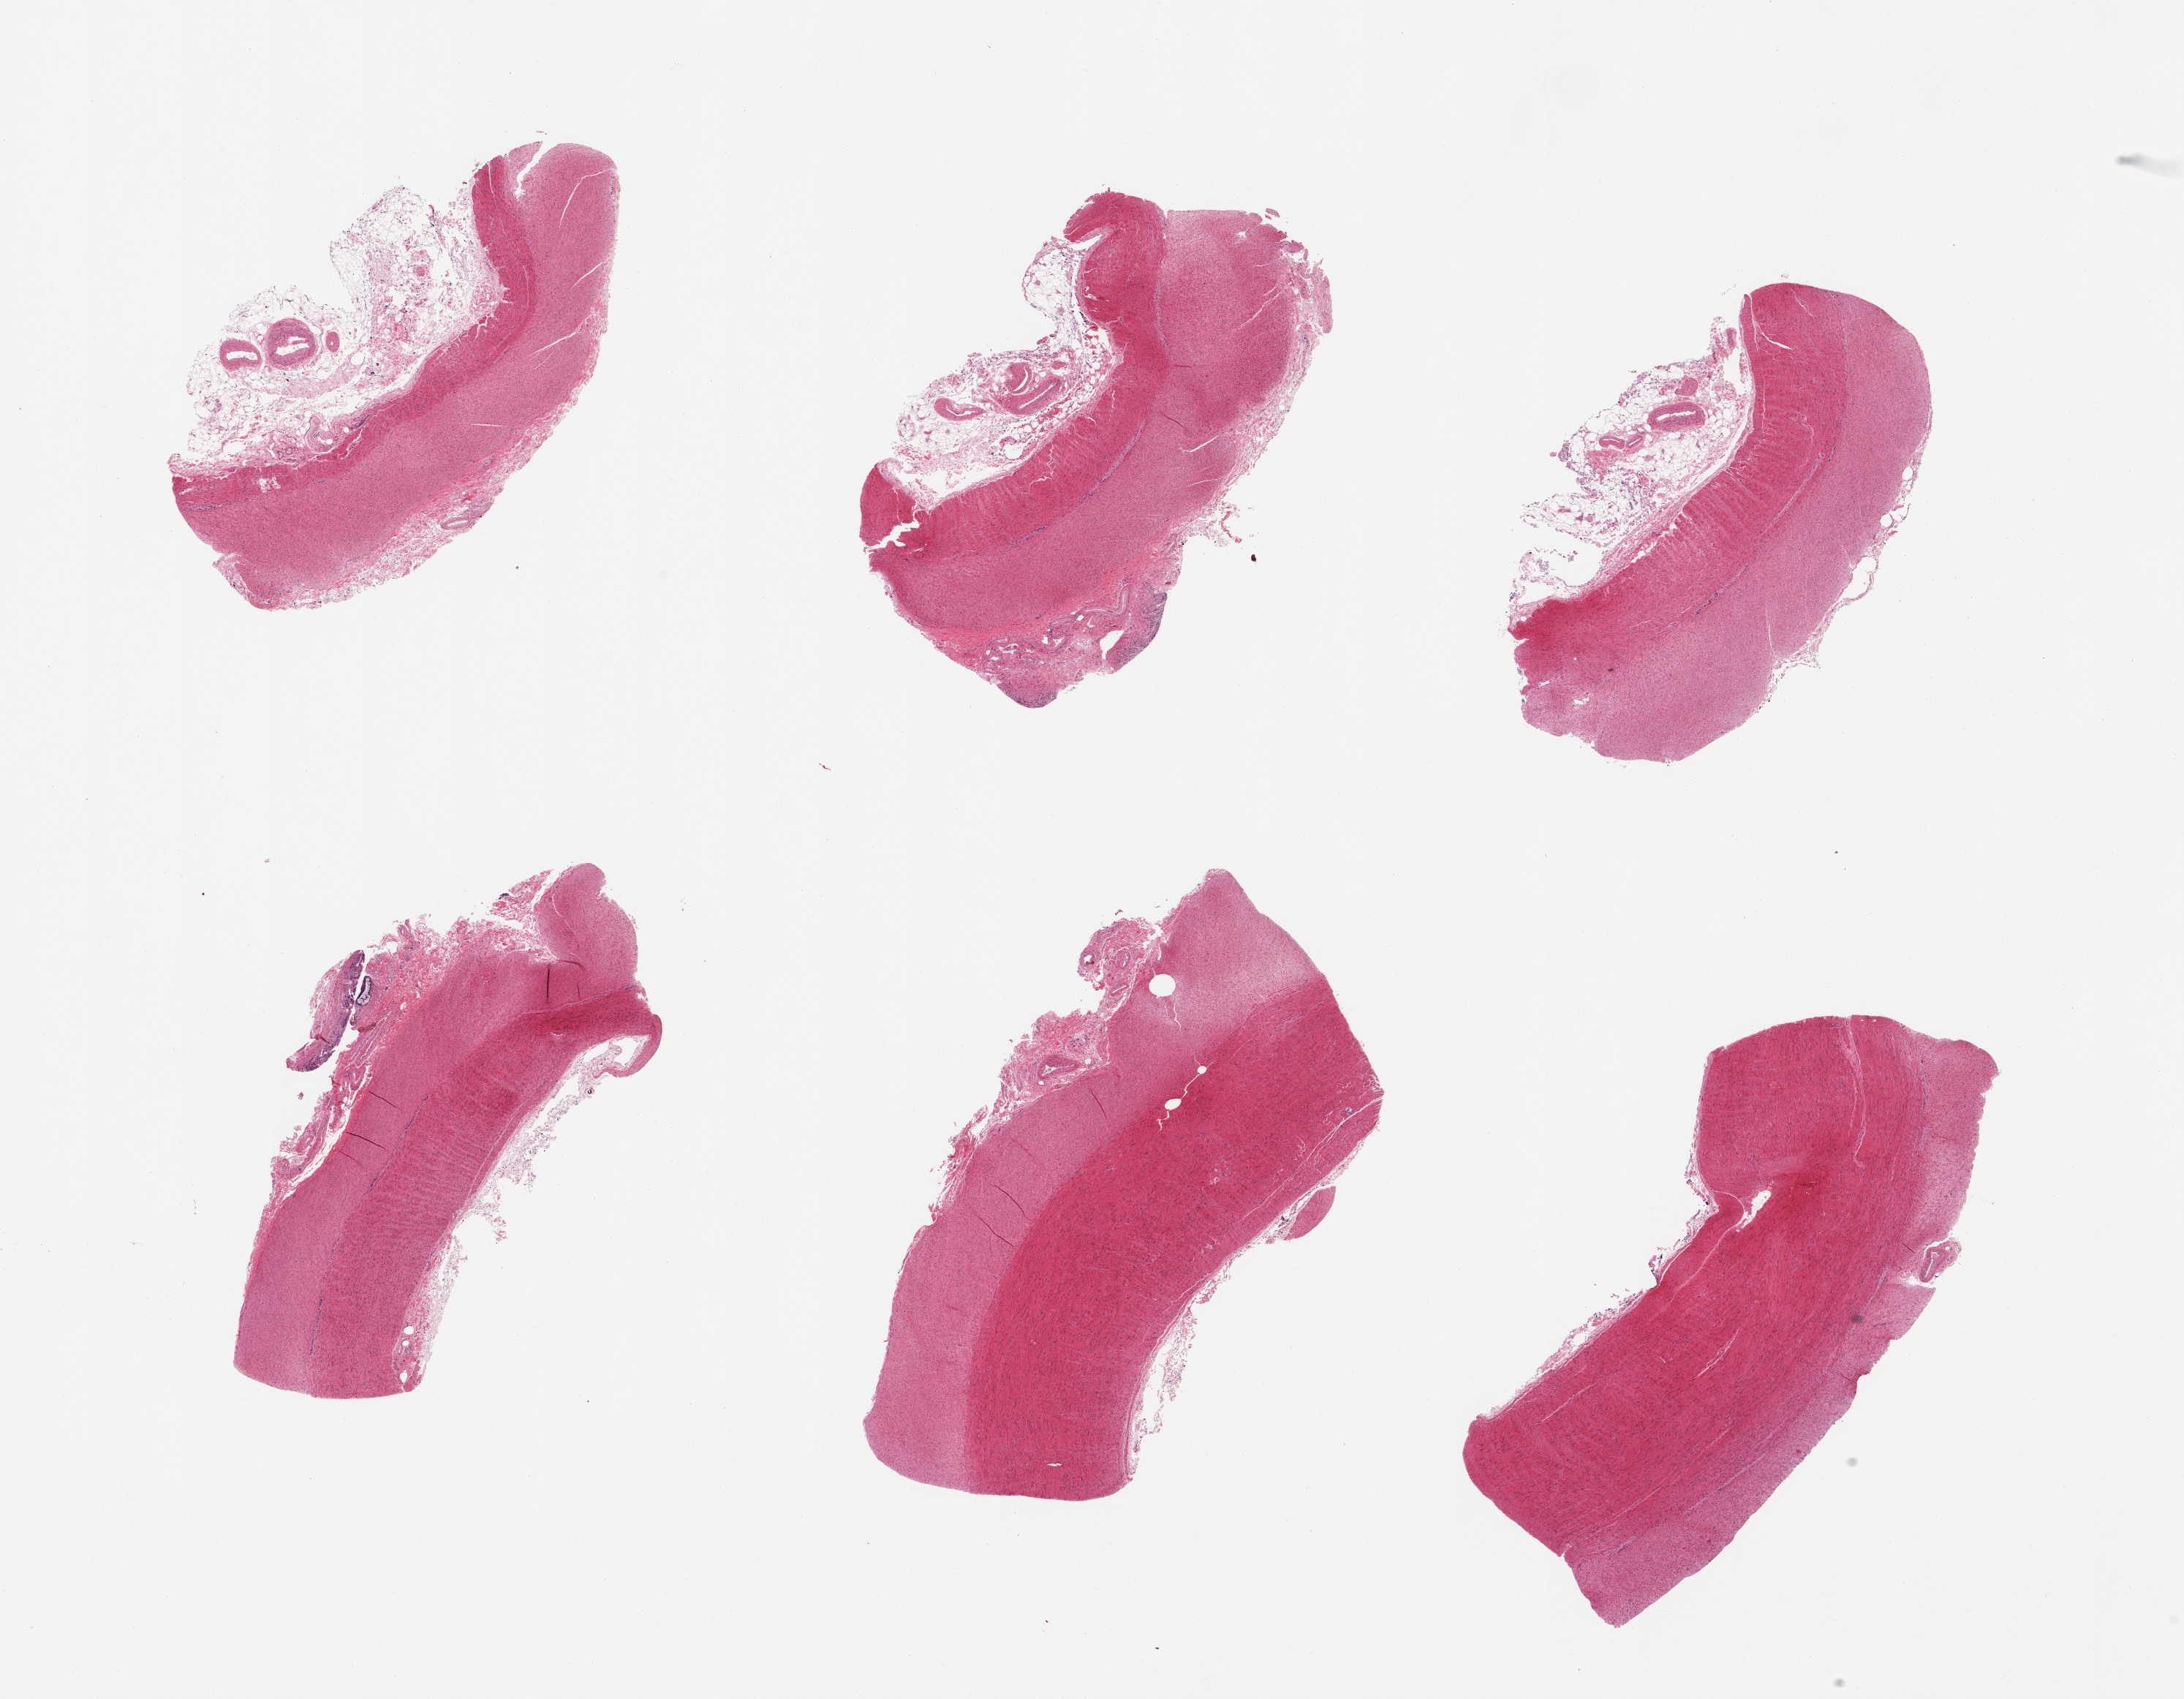
Digitized hematoxylin and eosin (H&E)-stained section, brightfield, a low-resolution overview of the entire scanned area, about 23.6 x 18.4 mm (slide scanned at 20x). PAXgene-fixed, paraffin-embedded tissue. Section of sigmoid colon (target tissue). Donor tissue sample. Male donor.
Pathologist's review note for this sample: 6 pieces; fatty submucosa occupies 30% in 3 of 6 pieces.